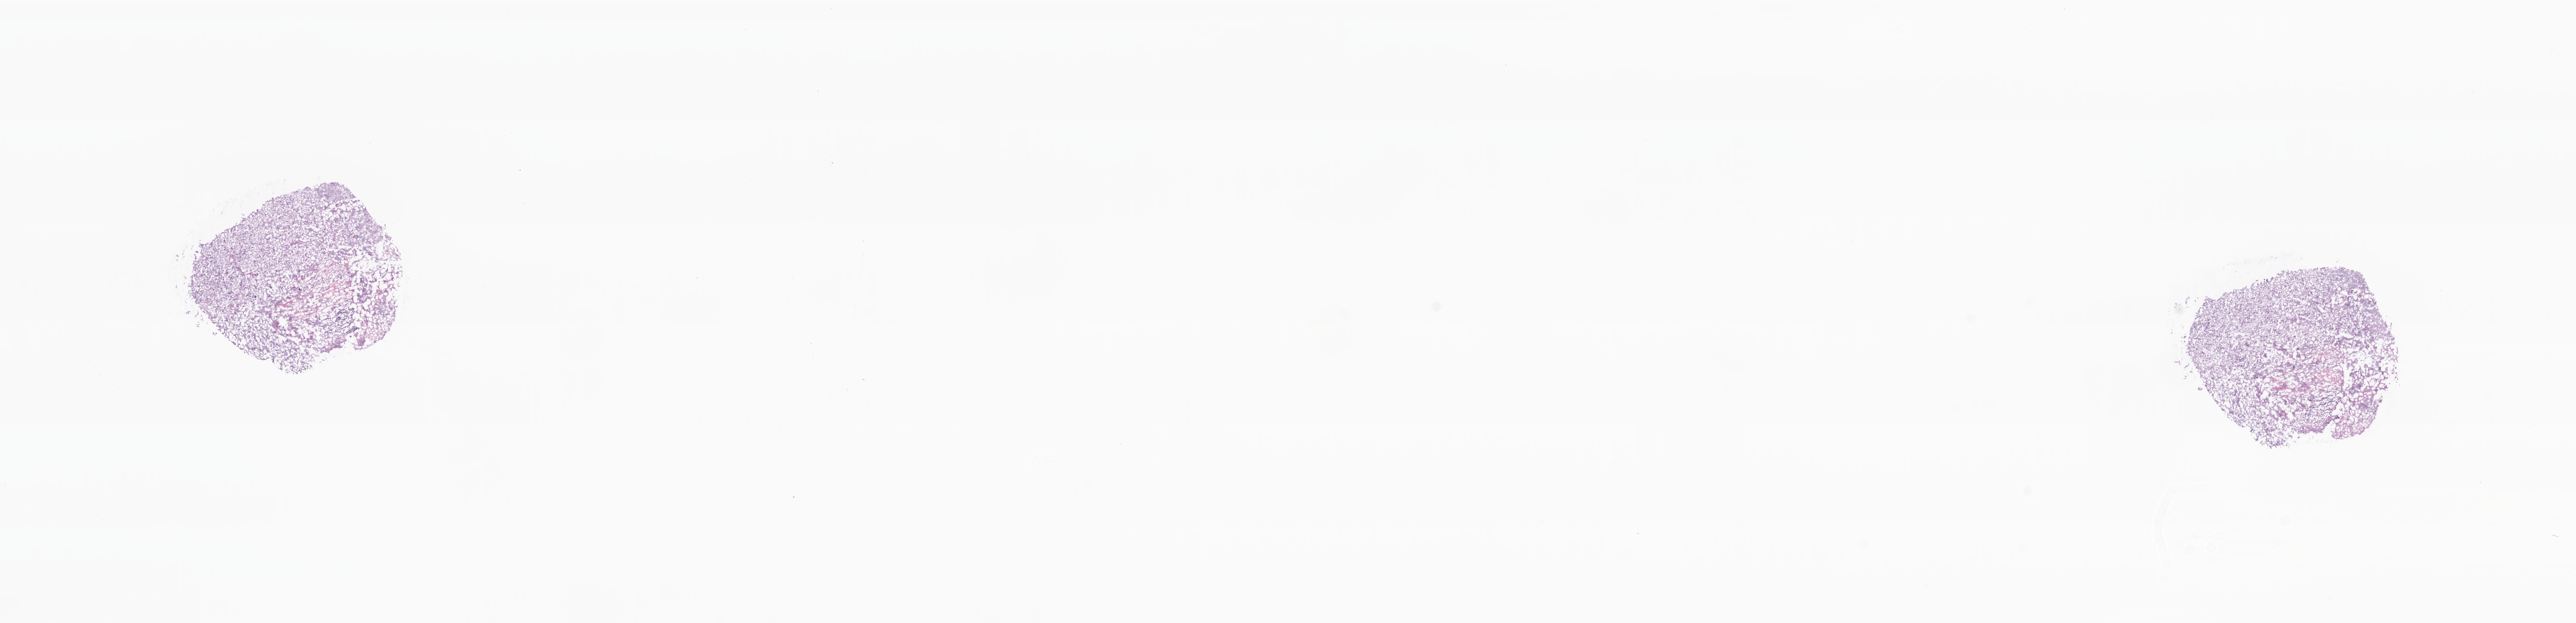
Digitized haematoxylin and eosin-stained section, low-resolution overview of the scanned area, about 27.1 x 6.6 mm; frozen section; specimen: primary tumor; anatomic site: bladder. Male patient. Pathologist review of this section (percent, as recorded): tumor cells 70%, tumor nuclei 80%.
Diagnosis: Transitional cell carcinoma, NOS.